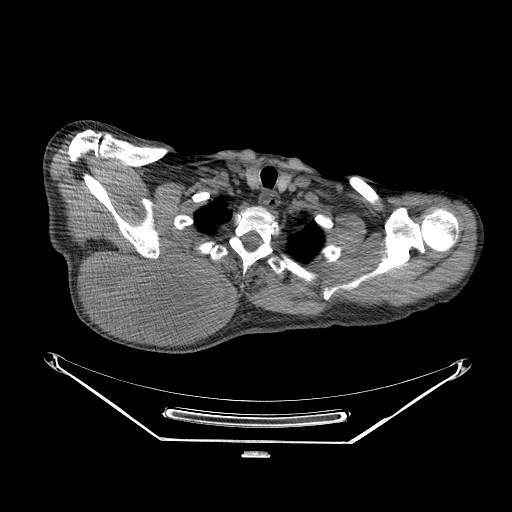
CT of an extremity soft-tissue mass (from a PET/CT study), one axial slice; slice 205 of 267 in the series (ordered by position); 140 kVp; soft-tissue window (W 400 / L 40 HU); 512 × 512 image matrix. Male patient. Case-level facts recorded for this patient, not image findings: histological type: pleiomorphic spindle cell undifferentiated; grade: high; site of the primary tumour: right parascapusular.
Structures marked on this image (expert contour drawn on MRI and transferred to this co-registered scan by the dataset authors):
- gross tumour volume including surrounding oedema: box from (x=82, y=244) to (x=236, y=330) px
- gross tumour volume (mass): (x=85, y=244)–(x=223, y=327)